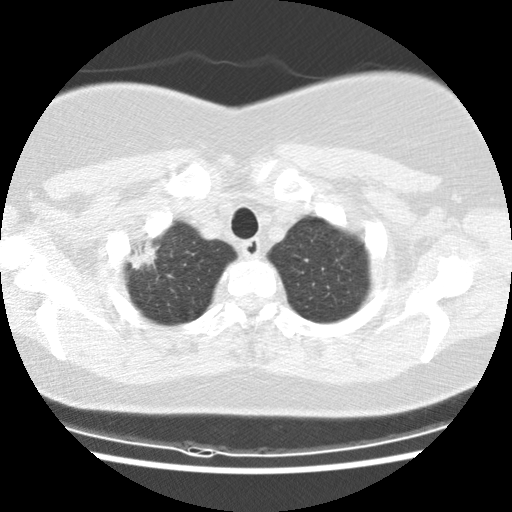
Low-dose screening chest CT, one axial slice. Slice 120 of 132 in the series (ordered by position). Reconstruction kernel STANDARD. 120 kVp. Lung window (W 1500 / L -600 HU). 2.5 mm slice thickness. 512 × 512 image matrix.
Outlined on this slice (outlined manually by an expert reader):
- lesion 1 (tumor, upper lobe of right lung): bounding box <132,245,159,270> (left, top, right, bottom; pixels)